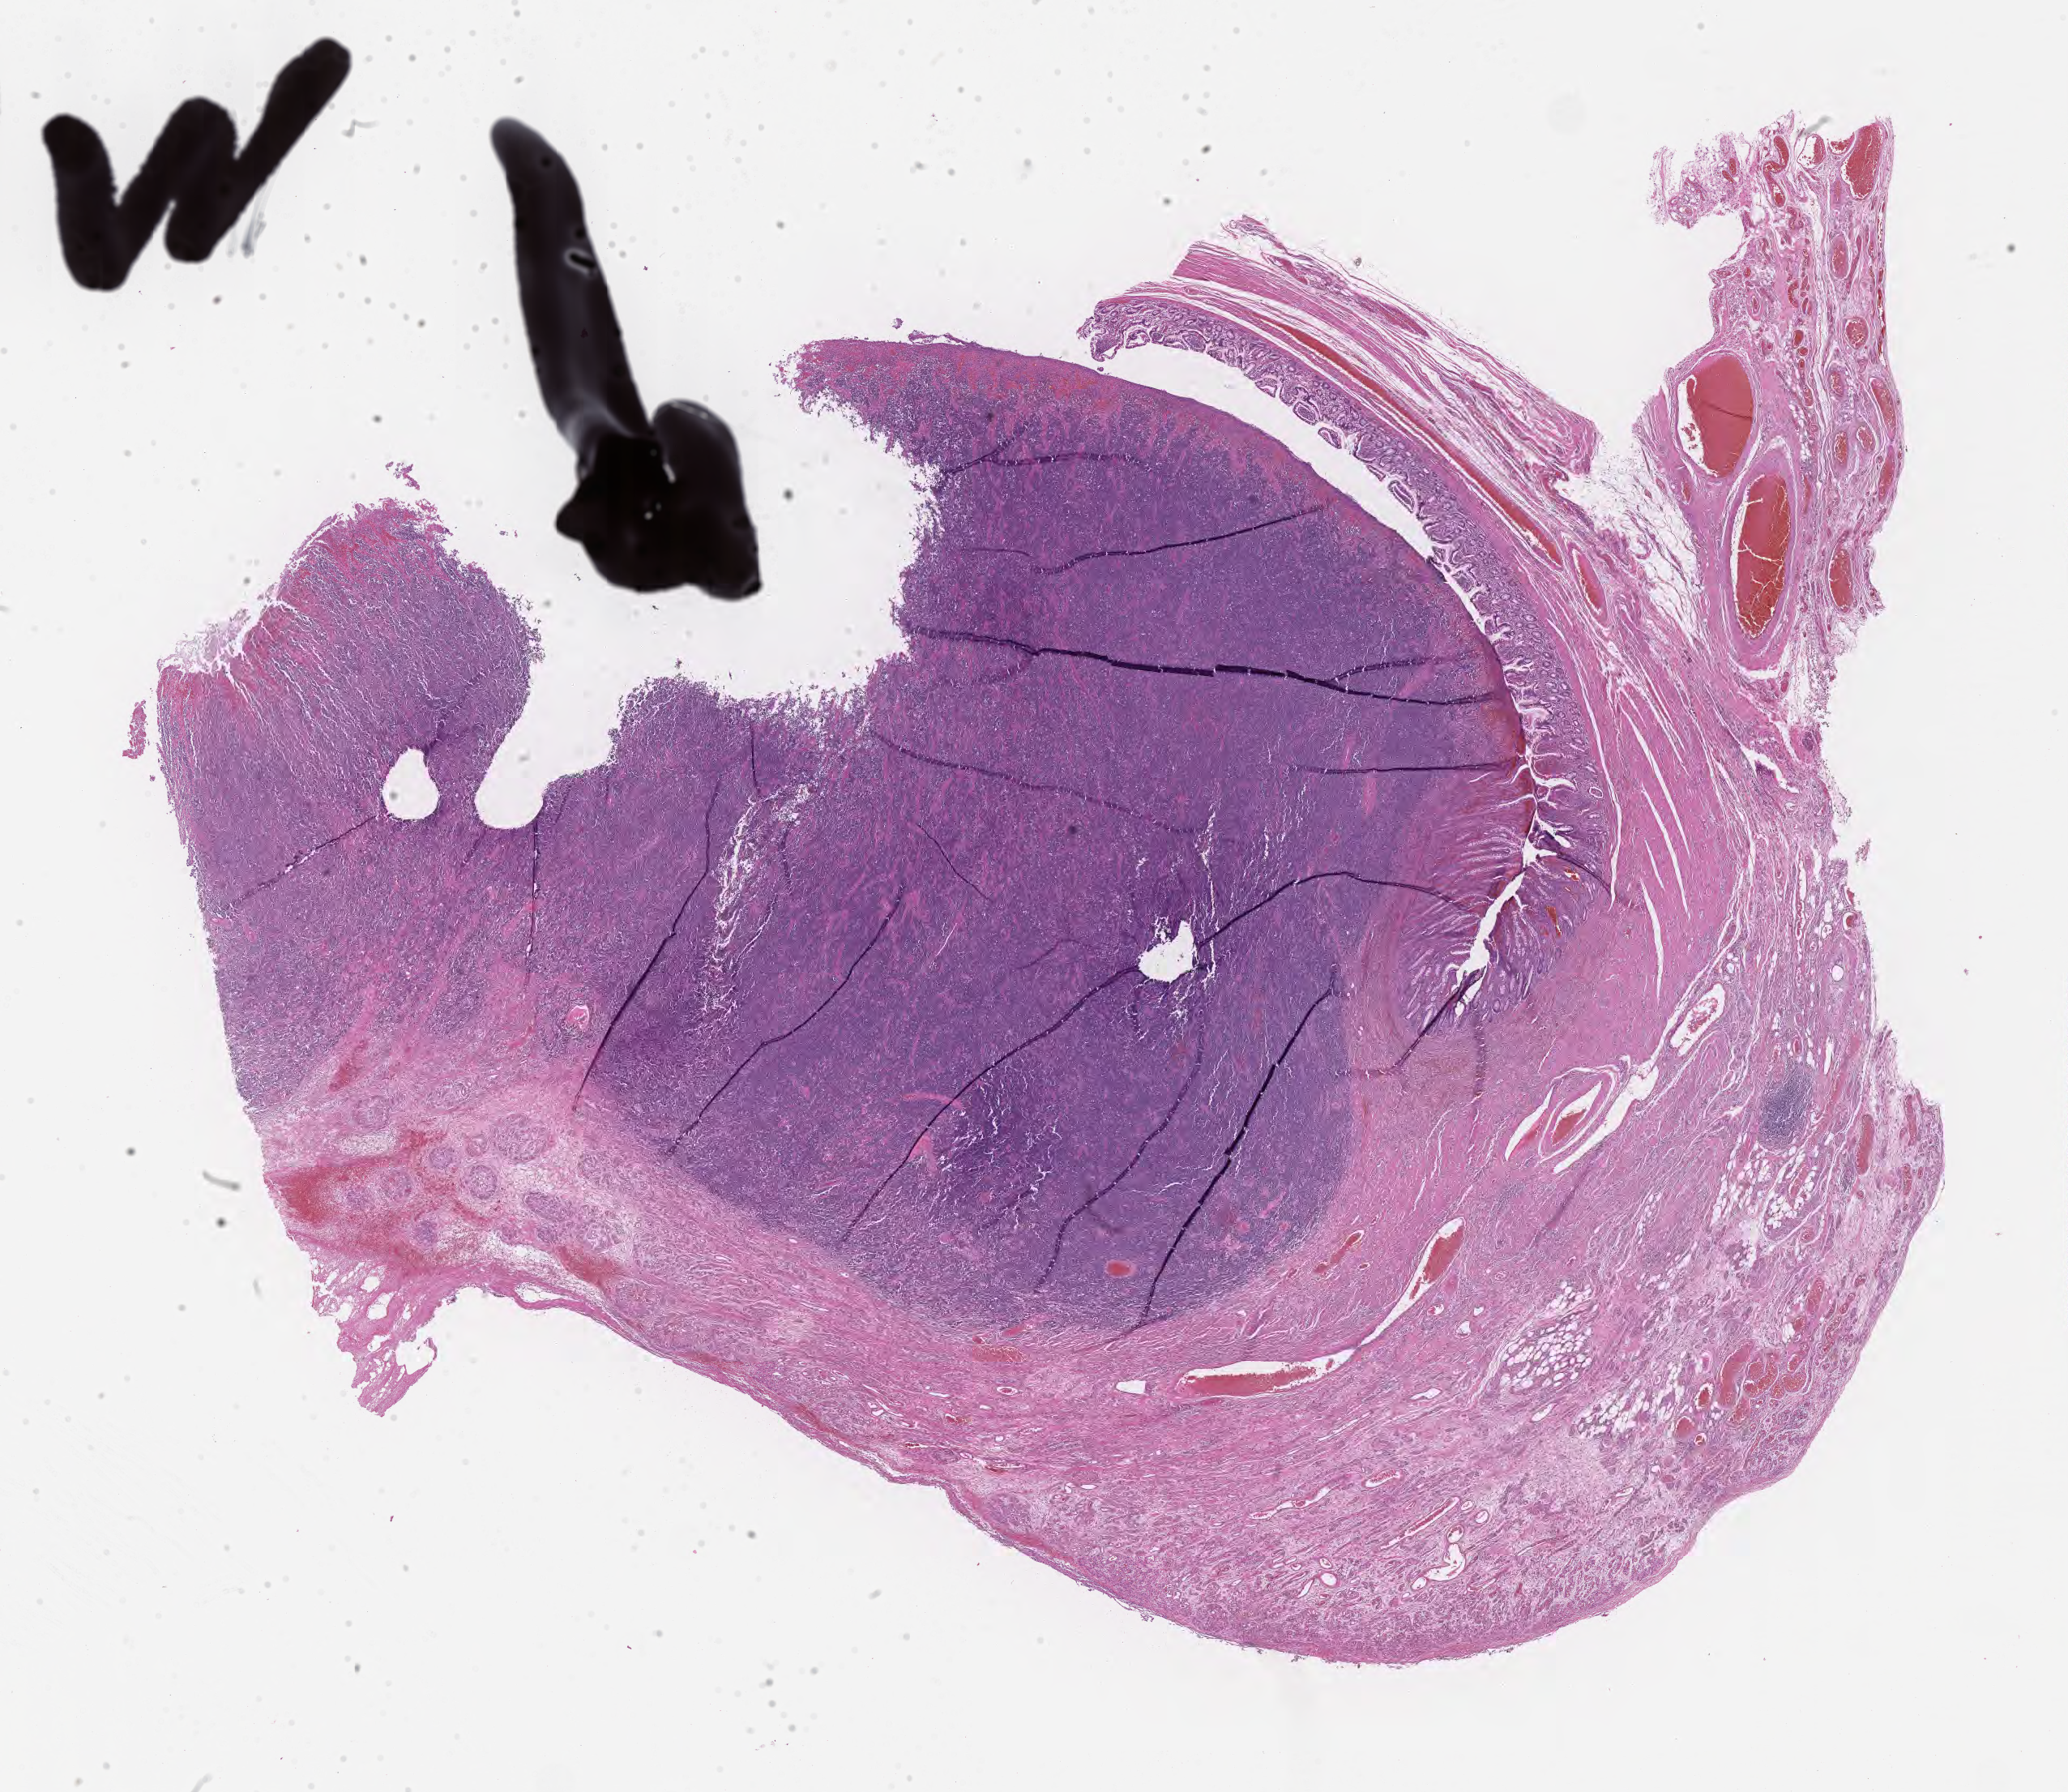
Digitized hematoxylin and eosin (H&E)-stained section, whole scanned area (about 20.6 x 17.9 mm) shown as a low-resolution overview. Tumor tissue. Patient male; aged 26.
Diagnosis: Burkitt lymphoma, NOS.